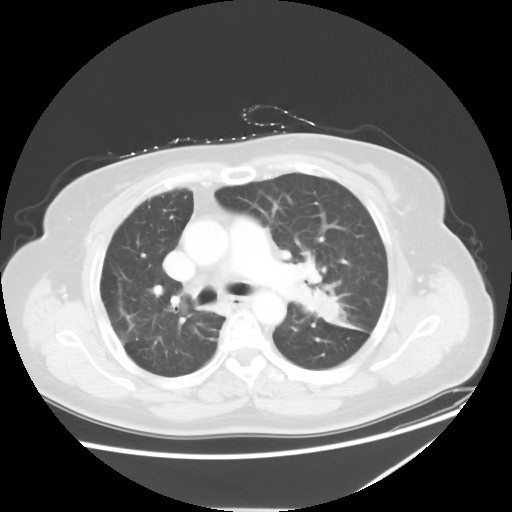
Chest CT, one axial slice; slice 35 of 54 in the series (ordered by position); reconstruction kernel STANDARD; lung window (W 1500 / L -600 HU); 5 mm slice thickness; 512 × 512 image matrix, field of view 384 × 384 mm. Female patient, age 61 years. From the clinical record (not read from this slice): clinical TNM (as recorded): T1c N3 M1.
Outlined on this slice (bounding box drawn by a radiologist):
- lung tumour (recorded histology: adenocarcinoma): bounding box (x1, y1, x2, y2) in pixels: (304, 284, 373, 337)